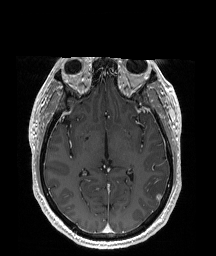
Brain MRI from a brain-tumour surgery series, one axial slice; position 105 of 192 along the scan axis; T1-weighted post-contrast; 1 mm slice thickness; 216 × 256 image matrix. Case-level facts recorded for this patient, not image findings: histopathology: Glioblastoma; WHO grade: 4; IDH mutation: no.
Outlined on this slice (manually delineated by an expert):
- tumour: bounding box (x1, y1, x2, y2) in pixels: (143, 175, 167, 203)